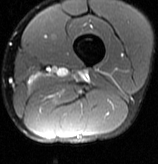
MRI of an extremity soft-tissue mass, one axial slice; position 13 of 70 along the scan axis; T2-weighted fat-saturated; MR volume resampled by the dataset authors to the PET/CT grid (not the native acquisition matrix); 3.27 mm slice thickness; 158 × 164 image matrix, field of view 154 × 160 mm. Male patient. Case-level facts recorded for this patient, not image findings: histological type: extraskeletal osteosarcoma; grade: high; site of the primary tumour: left adductur.
Structures marked on this image (expert contour drawn on MRI and transferred to this co-registered scan by the dataset authors):
- gross tumour volume (mass): box from (x=81, y=73) to (x=87, y=79) px